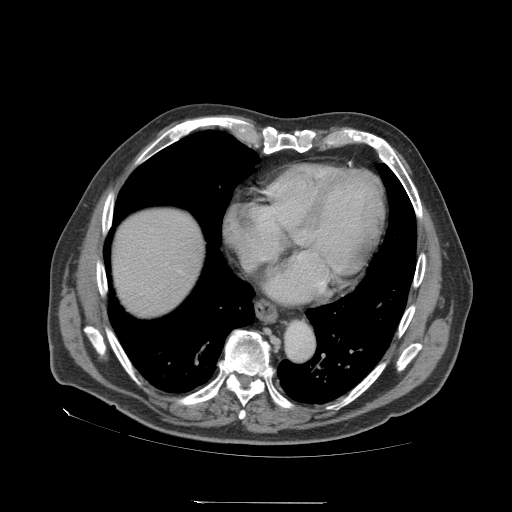
Contrast-enhanced abdominal CT (liver protocol), one axial slice. Slice 70 of 83 in the series (ordered by position). Reconstruction kernel STANDARD. Soft-tissue window (W 400 / L 40 HU). 2.5 mm slice thickness. 512 × 512 image matrix, field of view 460 × 460 mm. From the clinical record (not read from this slice): diagnosis: hepatocellular carcinoma (patient treated with transarterial chemoembolisation; whether this scan precedes or follows treatment is not stated here); TNM stage (as recorded): Stage-I; Child-Pugh class: A; tumour nodularity: uninodular.
Annotated regions visible in this slice (semi-automatically segmented with operator editing):
- liver parenchyma outside the tumour (the mass and vessels are separate outlines, so this box may not span the whole liver): bounding box <112,210,204,314> (left, top, right, bottom; pixels)